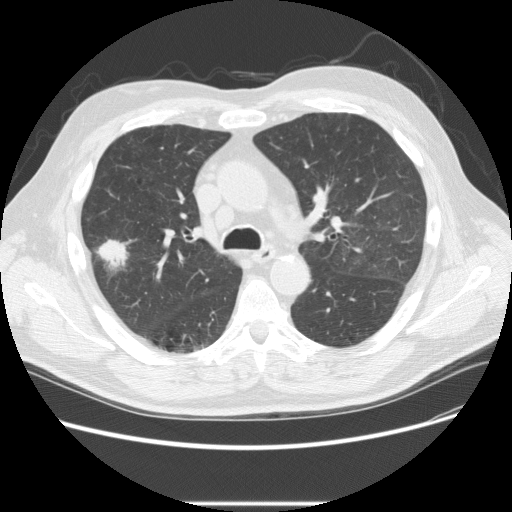
Low-dose screening chest CT, one axial slice. Slice 151 of 233 in the series (ordered by position). Reconstruction kernel STANDARD. Lung window (W 1500 / L -600 HU). 2.5 mm slice thickness. 512 × 512 image matrix, field of view 380 × 380 mm.
Structures marked on this image (manually delineated by an expert):
- lesion 2 (tumor, upper lobe of right lung): bounding box (x1, y1, x2, y2) in pixels: (96, 239, 129, 272)